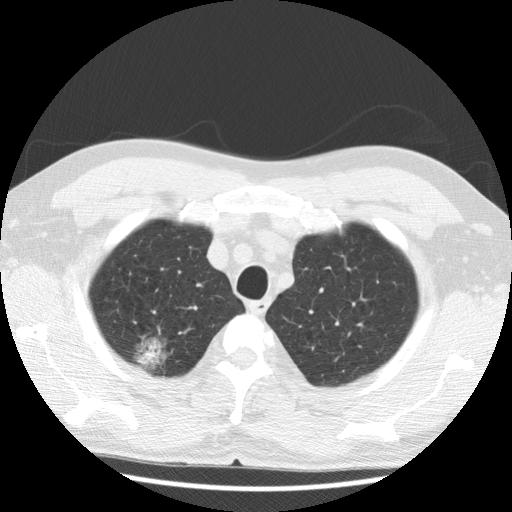
Low-dose screening chest CT, one axial slice; position 100 of 122 along the scan axis; 120 kVp; lung window (W 1500 / L -600 HU); 2.5 mm slice thickness; 512 × 512 image matrix, field of view 350 × 350 mm.
Outlined on this slice (outlined manually by an expert reader):
- lesion 1 (tumor, upper lobe of right lung): box from (x=139, y=343) to (x=160, y=364) px